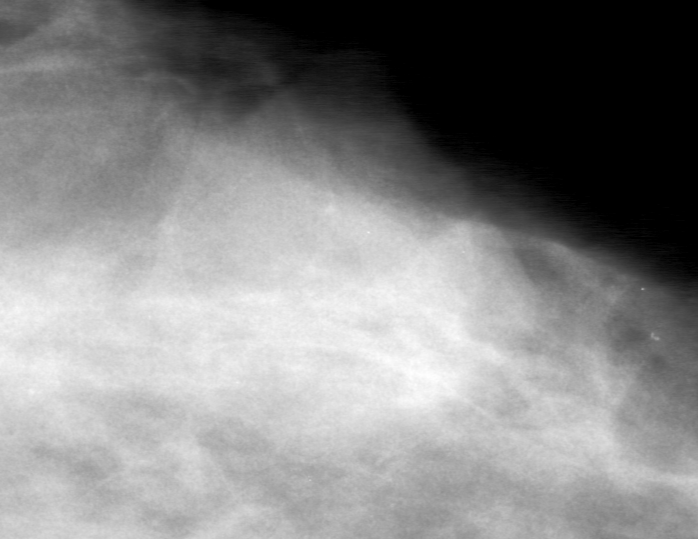
Region of interest cut from a scanned film mammogram (one marked finding), left breast, CC view.
Finding: mass, shape round, margins obscured; BI-RADS assessment category 0; pathology result (as recorded, not read from the image): benign.